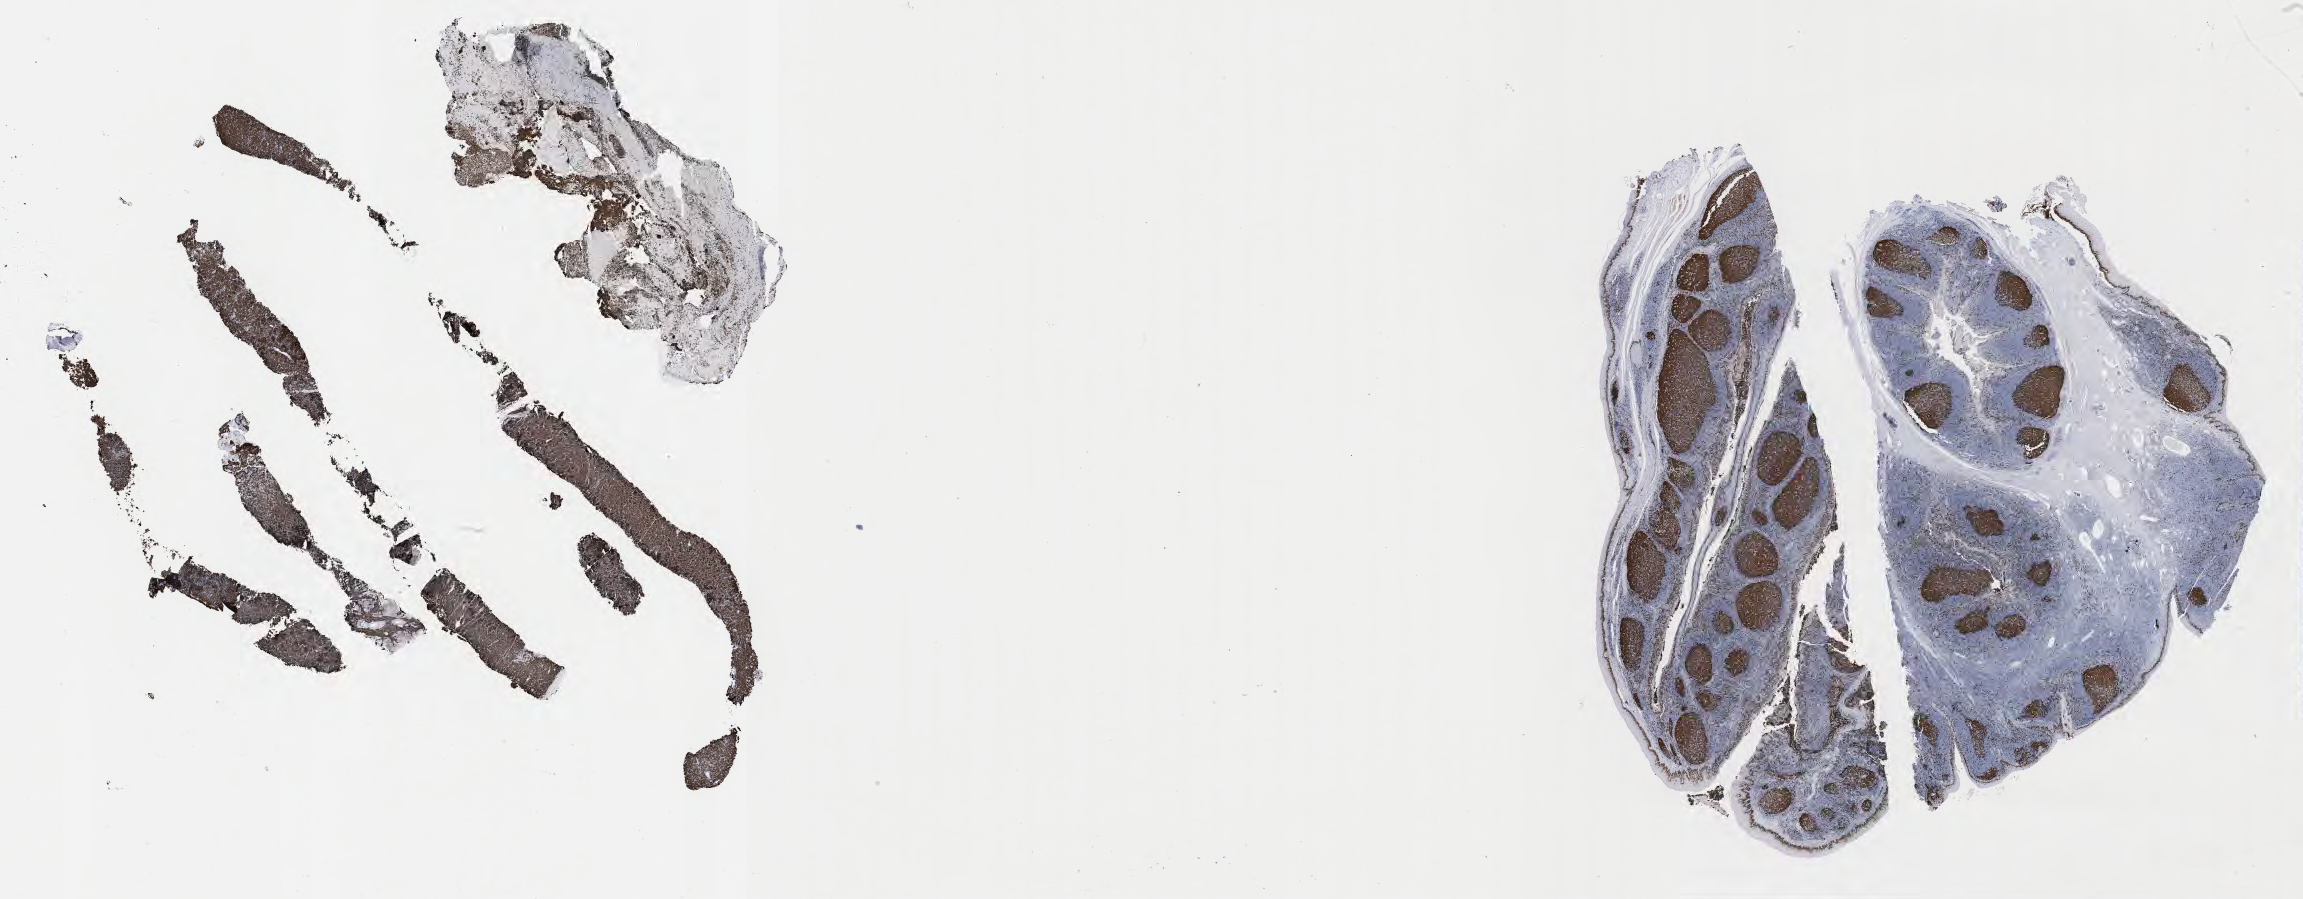
IHC for Ki-67, whole-slide image — shown as a low-resolution overview of the whole scanned area (about 37.2 x 14.5 mm). Tumor tissue. Patient: male, age 29 years.
- histologic diagnosis: Burkitt lymphoma, NOS